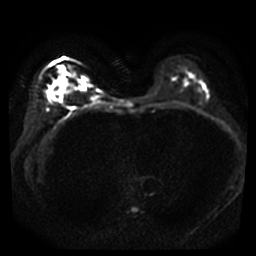
Breast MRI, one axial slice; slice 18 of 40 in the series (ordered by position); diffusion-weighted series; image 2 of 4 stored at this slice position (different b-values; order by instance number); 3 T; 5 mm slice thickness; 256 × 256 image matrix, field of view 320 × 320 mm. Female patient.
Structures marked on this image (manually delineated by an expert):
- tumour on diffusion-weighted imaging: bounding box (x1, y1, x2, y2) in pixels: (50, 75, 66, 97)